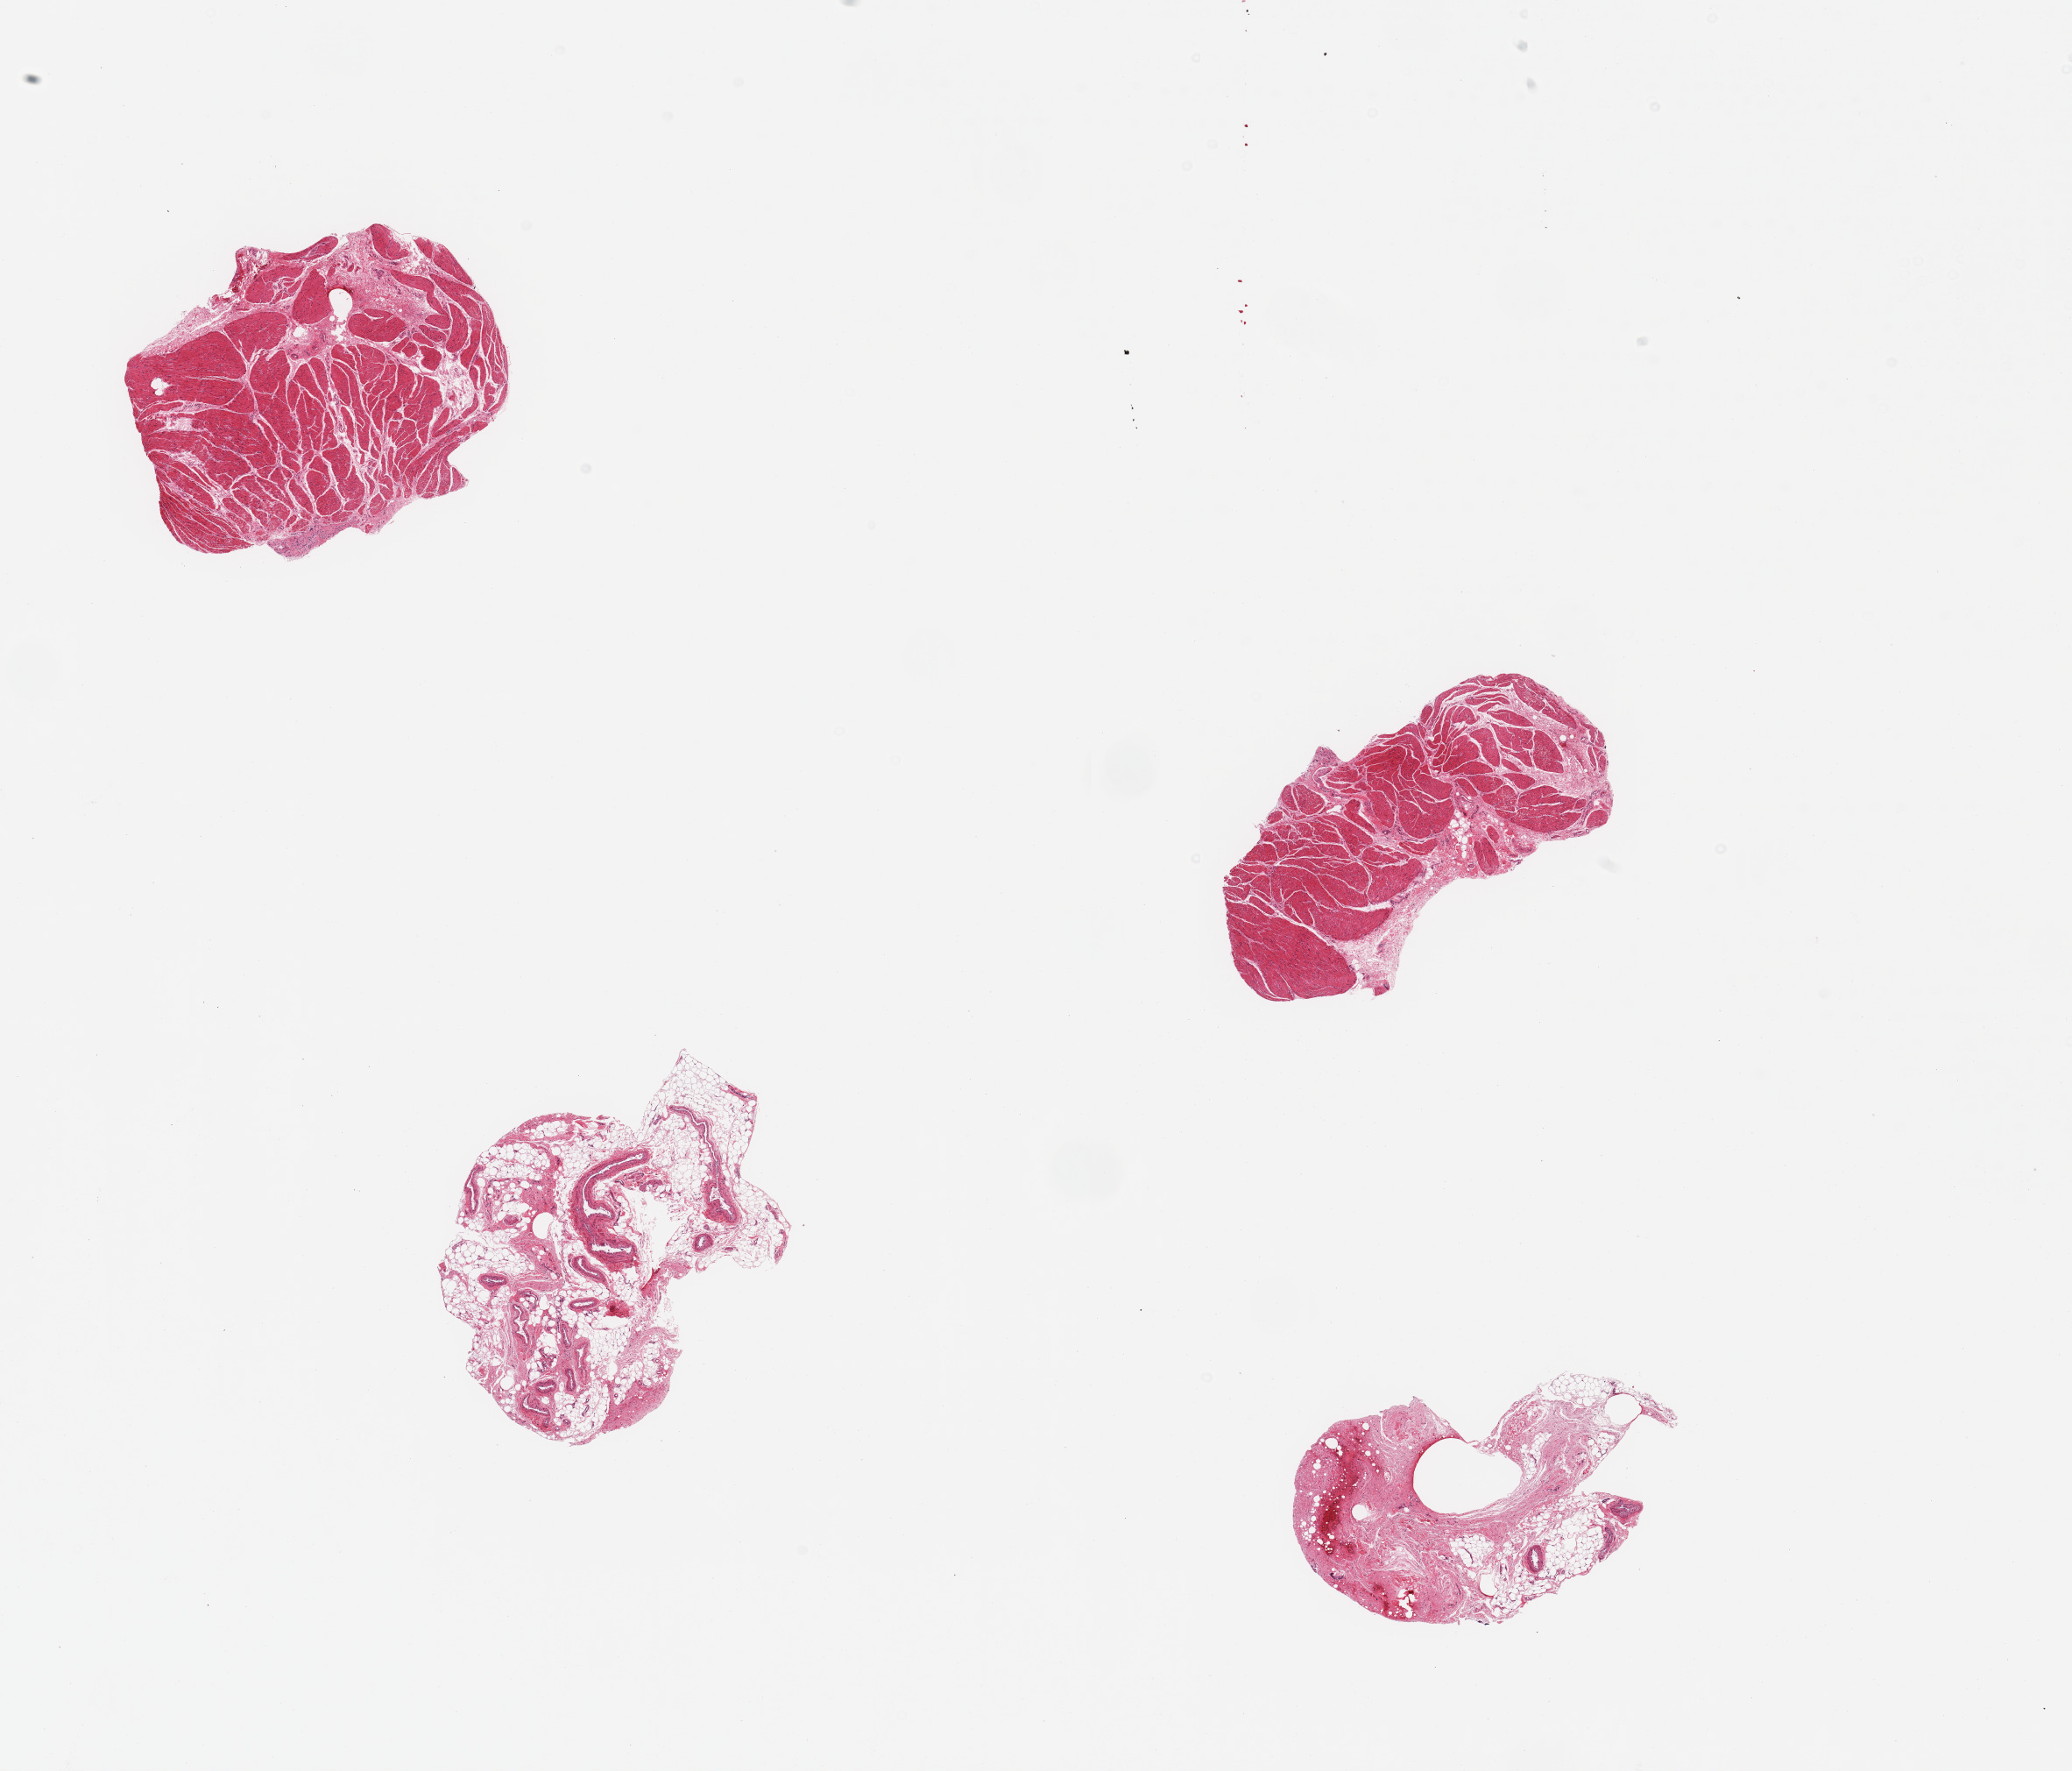
Whole-slide image, haematoxylin and eosin stain — low-resolution overview of the scanned area, about 18.7 x 16.0 mm. PAXgene-fixed, paraffin-embedded tissue. Target tissue: esophageal muscle. Donor tissue sample. Donor: female.
- pathologist's review note for this sample: 4 small pieces, 2 are muscle, 2 are fat